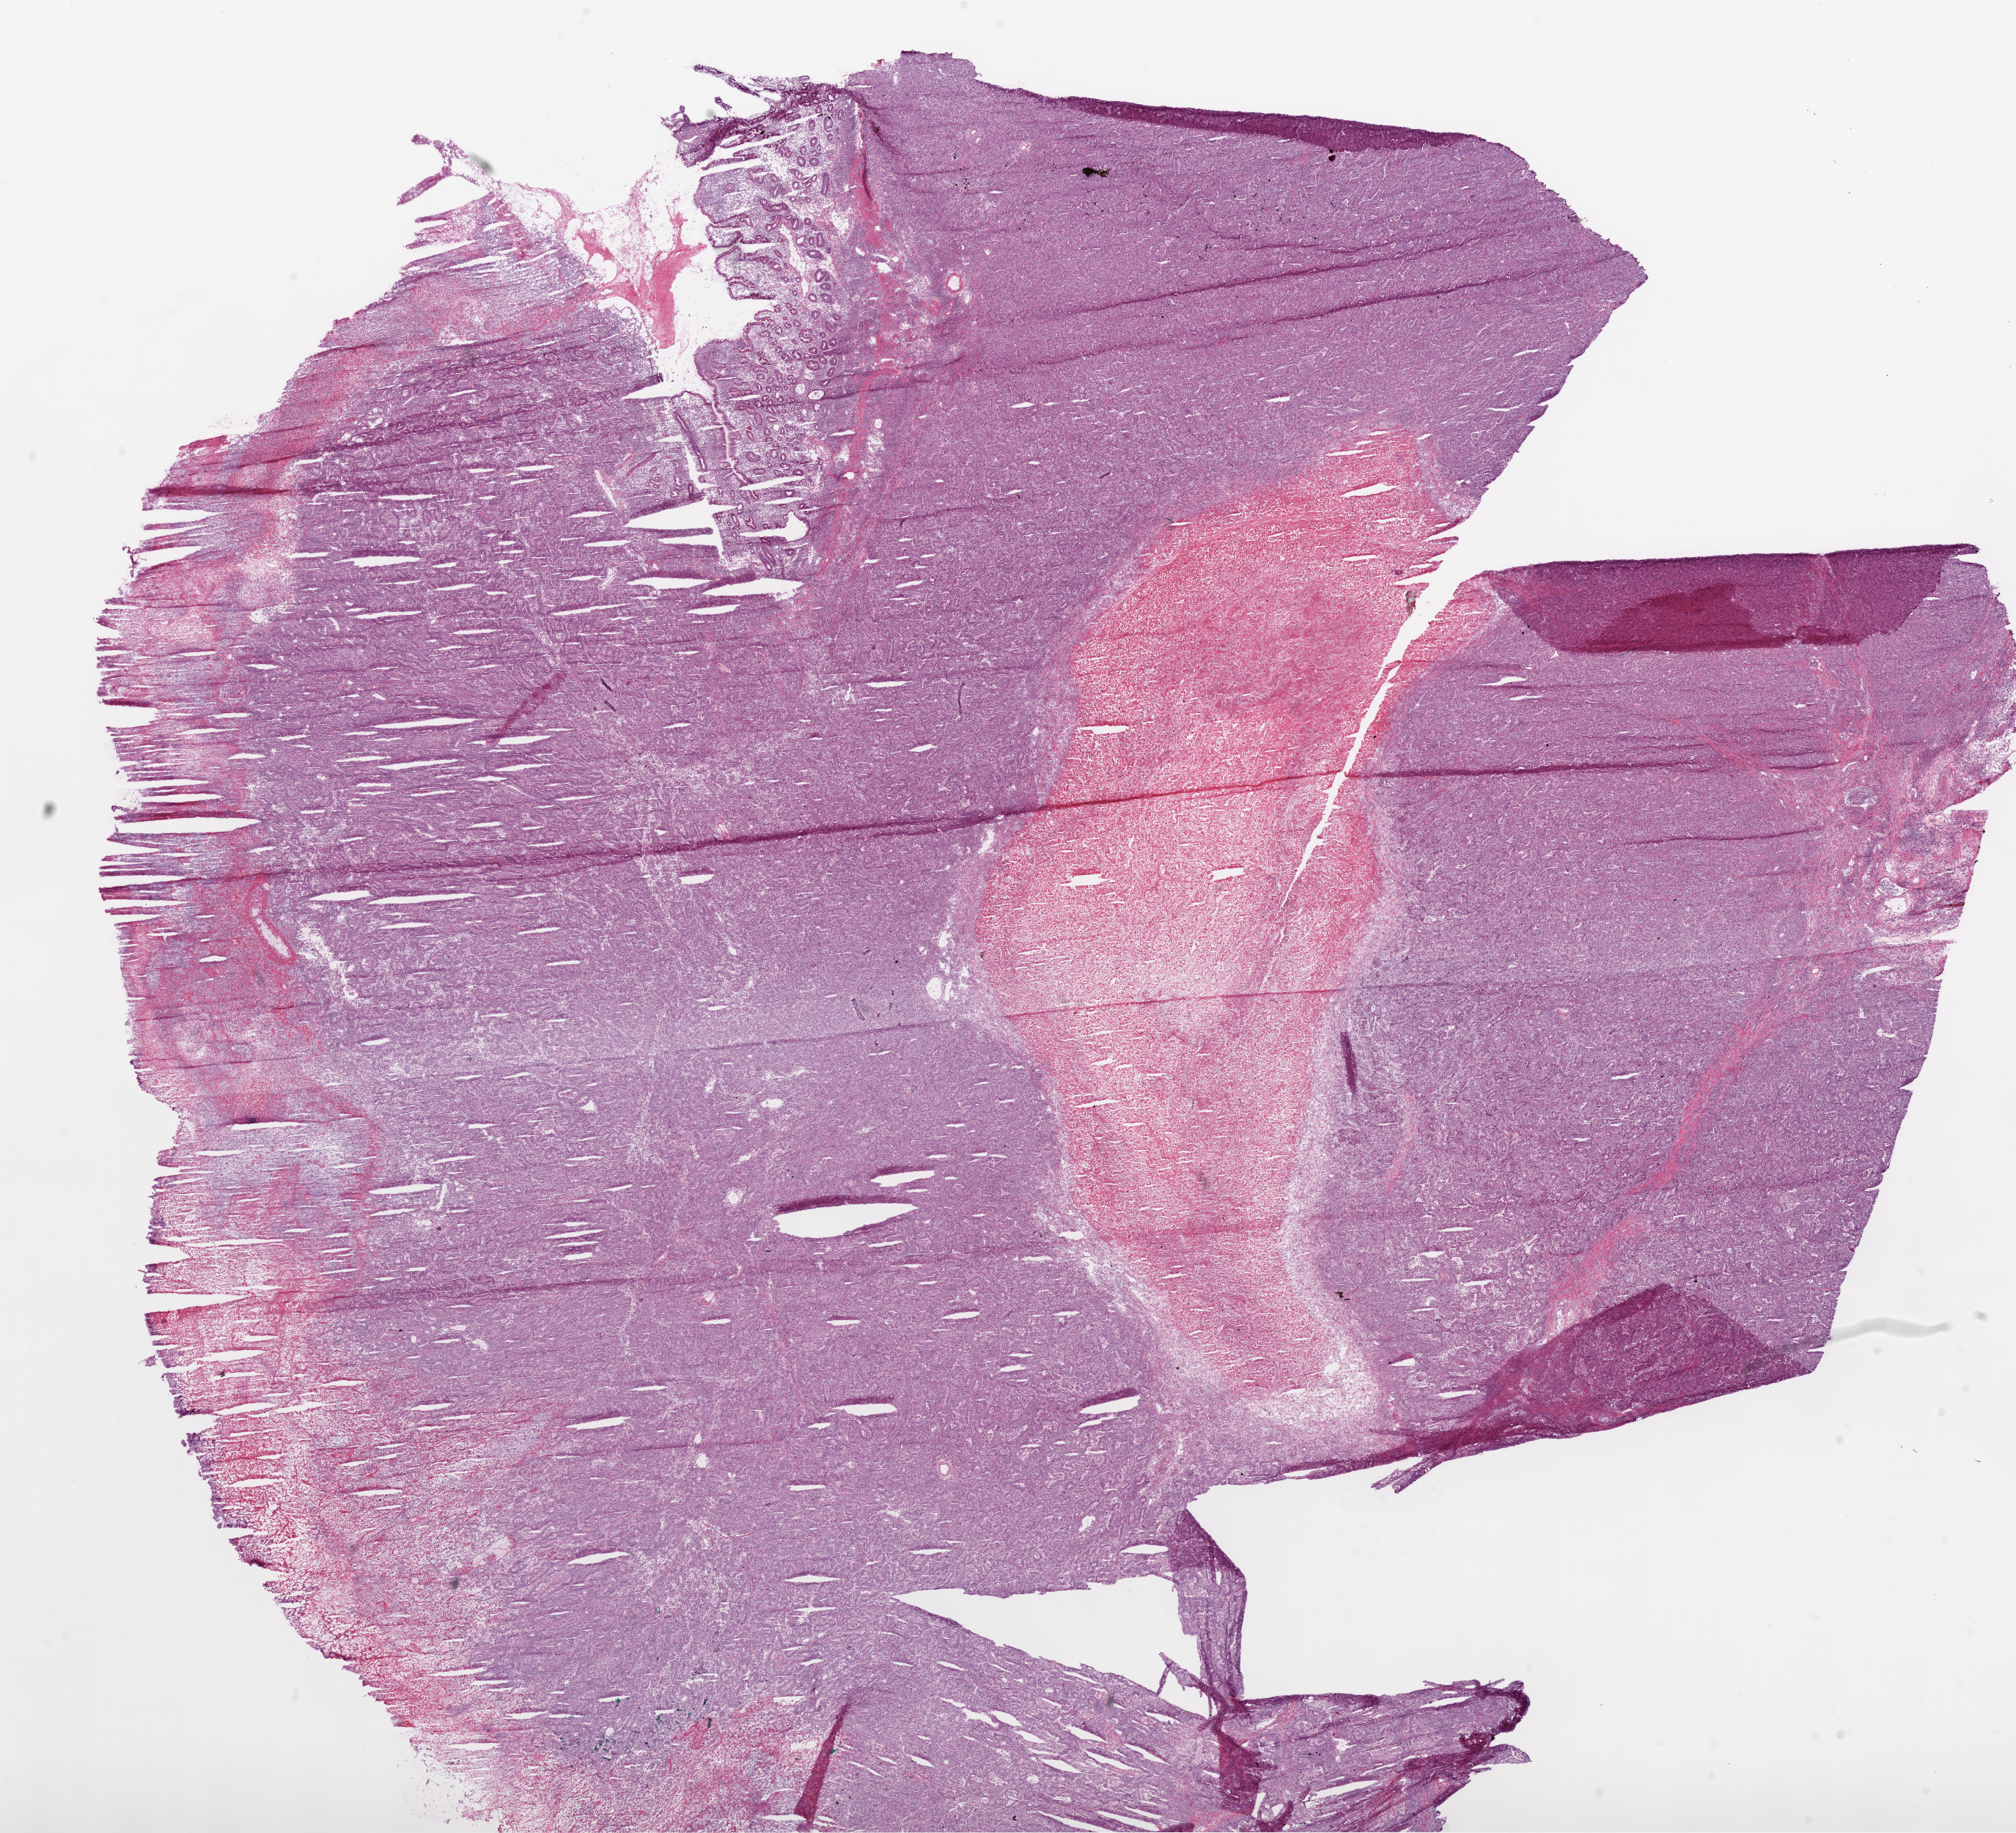
Whole-slide histology image, Hematoxylin and eosin (H&E) stained — low-resolution overview of the scanned area, about 22.1 x 20.1 mm. Frozen section from the bottom of the tissue portion. Stomach, primary tumour sample. Female, age 80 years at initial diagnosis. Histologic grade: G3 (poorly differentiated). Slide review estimates, as recorded: tumour cells 67%, tumour nuclei 70%, normal cells 5%, stromal cells 10%, necrosis 18%.
- histologic diagnosis: Adenocarcinoma, NOS (body of stomach)
- AJCC pathologic stage: IIIA (6th edition)
- TNM: T3 N1 M0